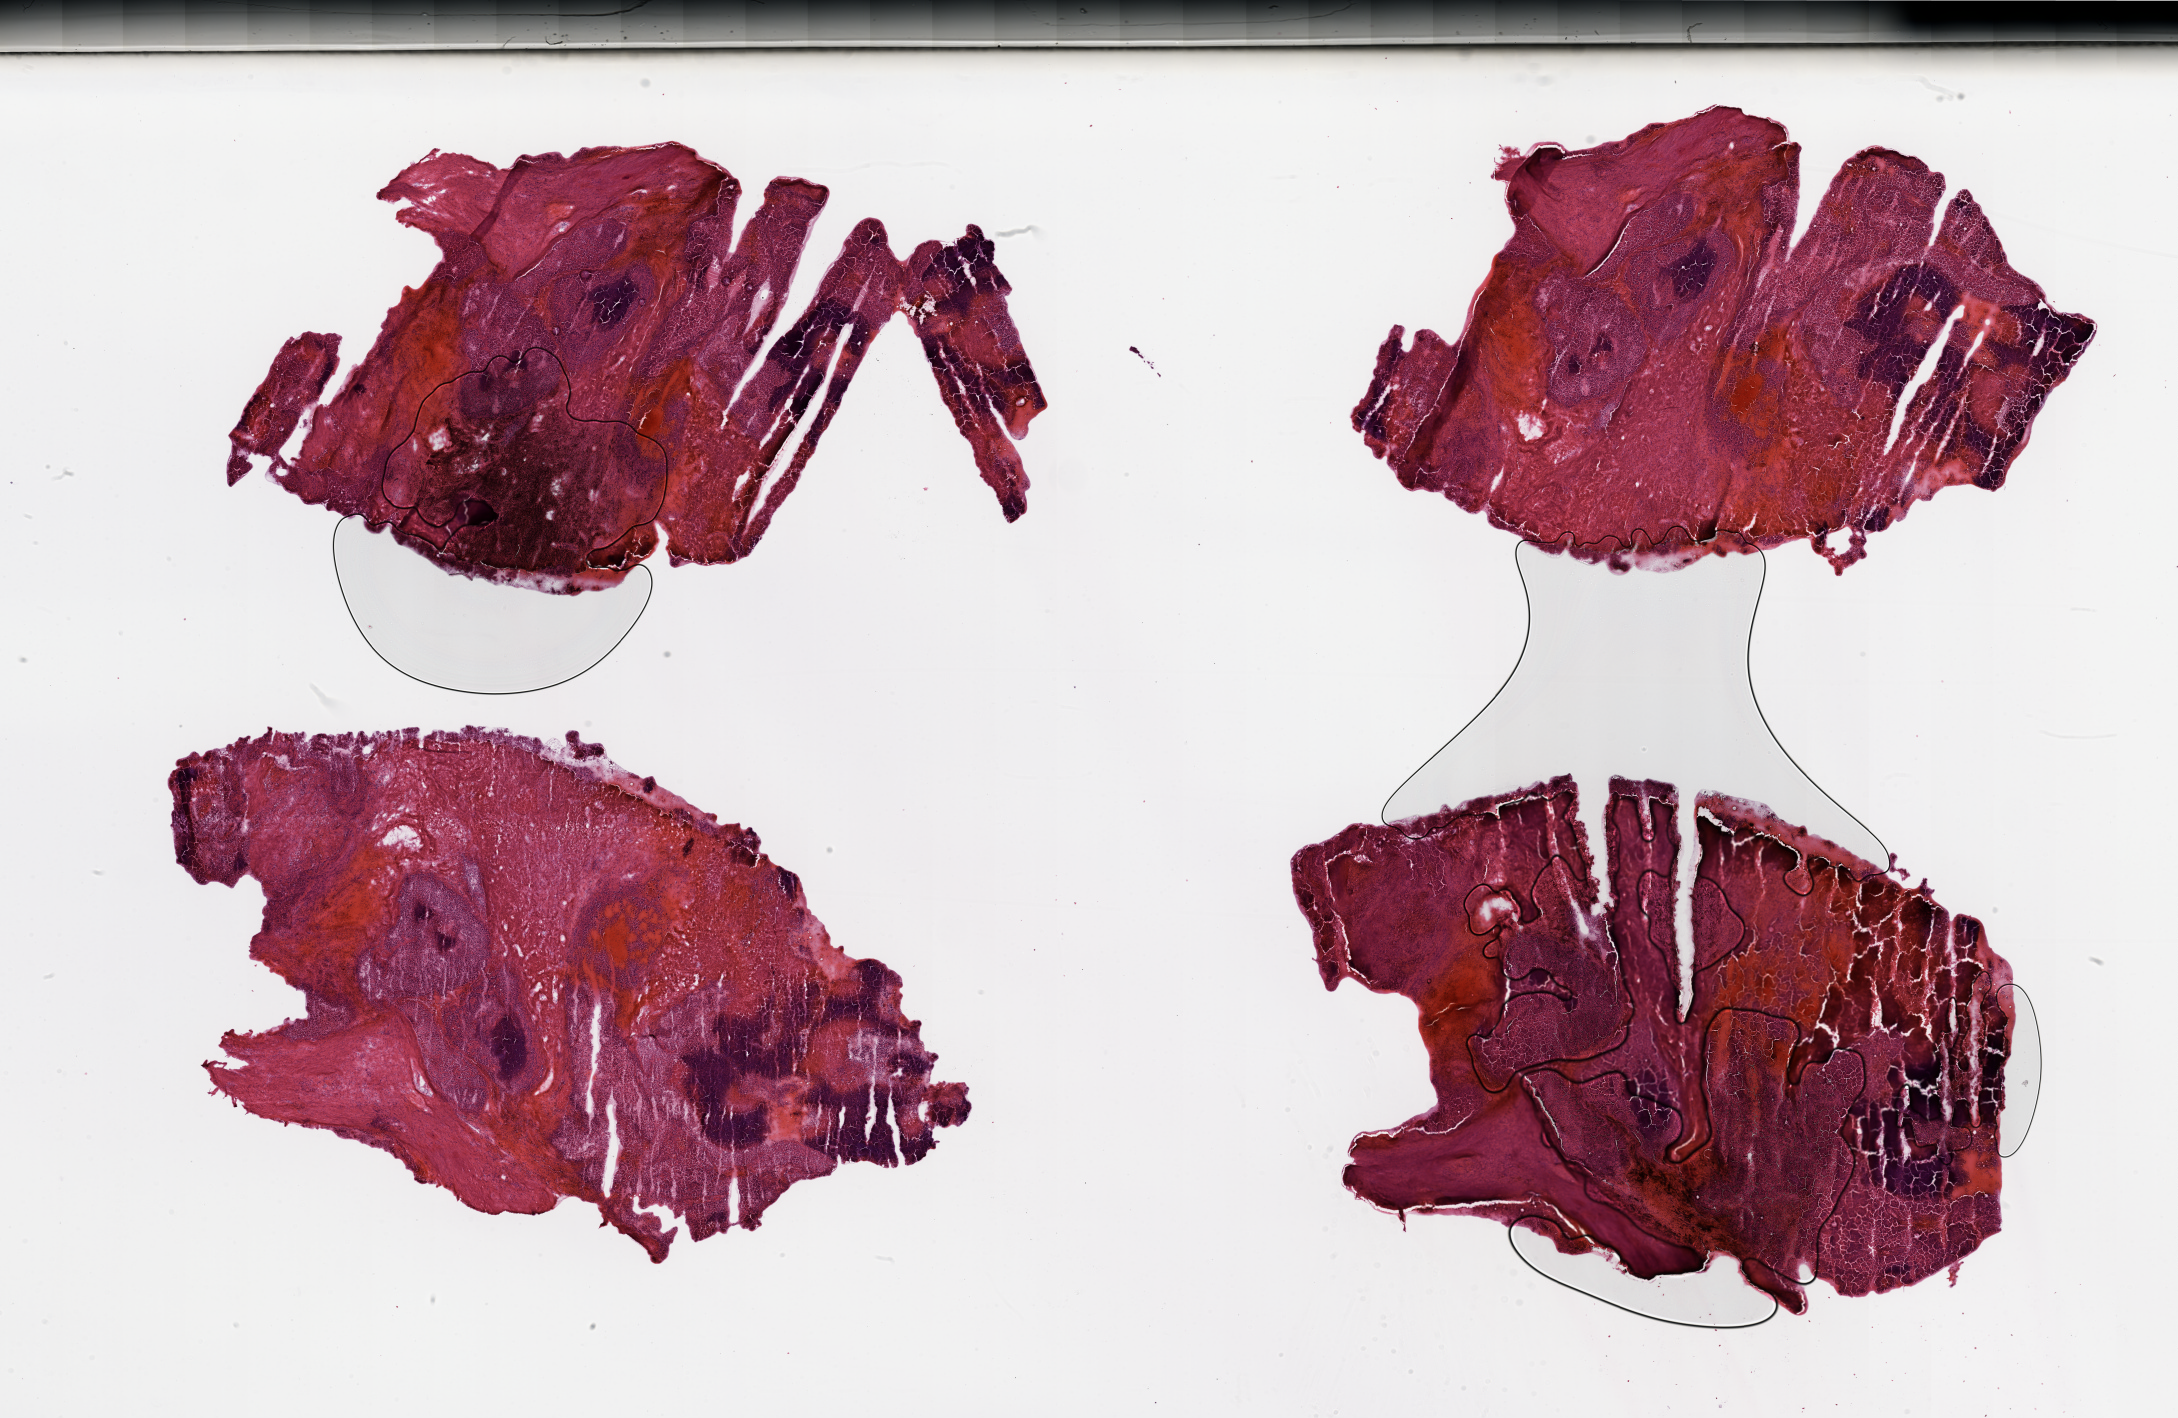
Whole-slide histology image, H&E-stained, low-resolution overview of the scanned area, about 34.5 x 22.4 mm, tumour tissue sample, sampled site: kidney. 84-year-old male patient. Histologic grade: G2 (moderately differentiated). Slide review estimates, as recorded: tumour nuclei 65%, necrosis 25%.
Histologic diagnosis: Renal cell carcinoma, NOS. AJCC pathologic stage: III. Primary tumour site (as recorded): upper pole.